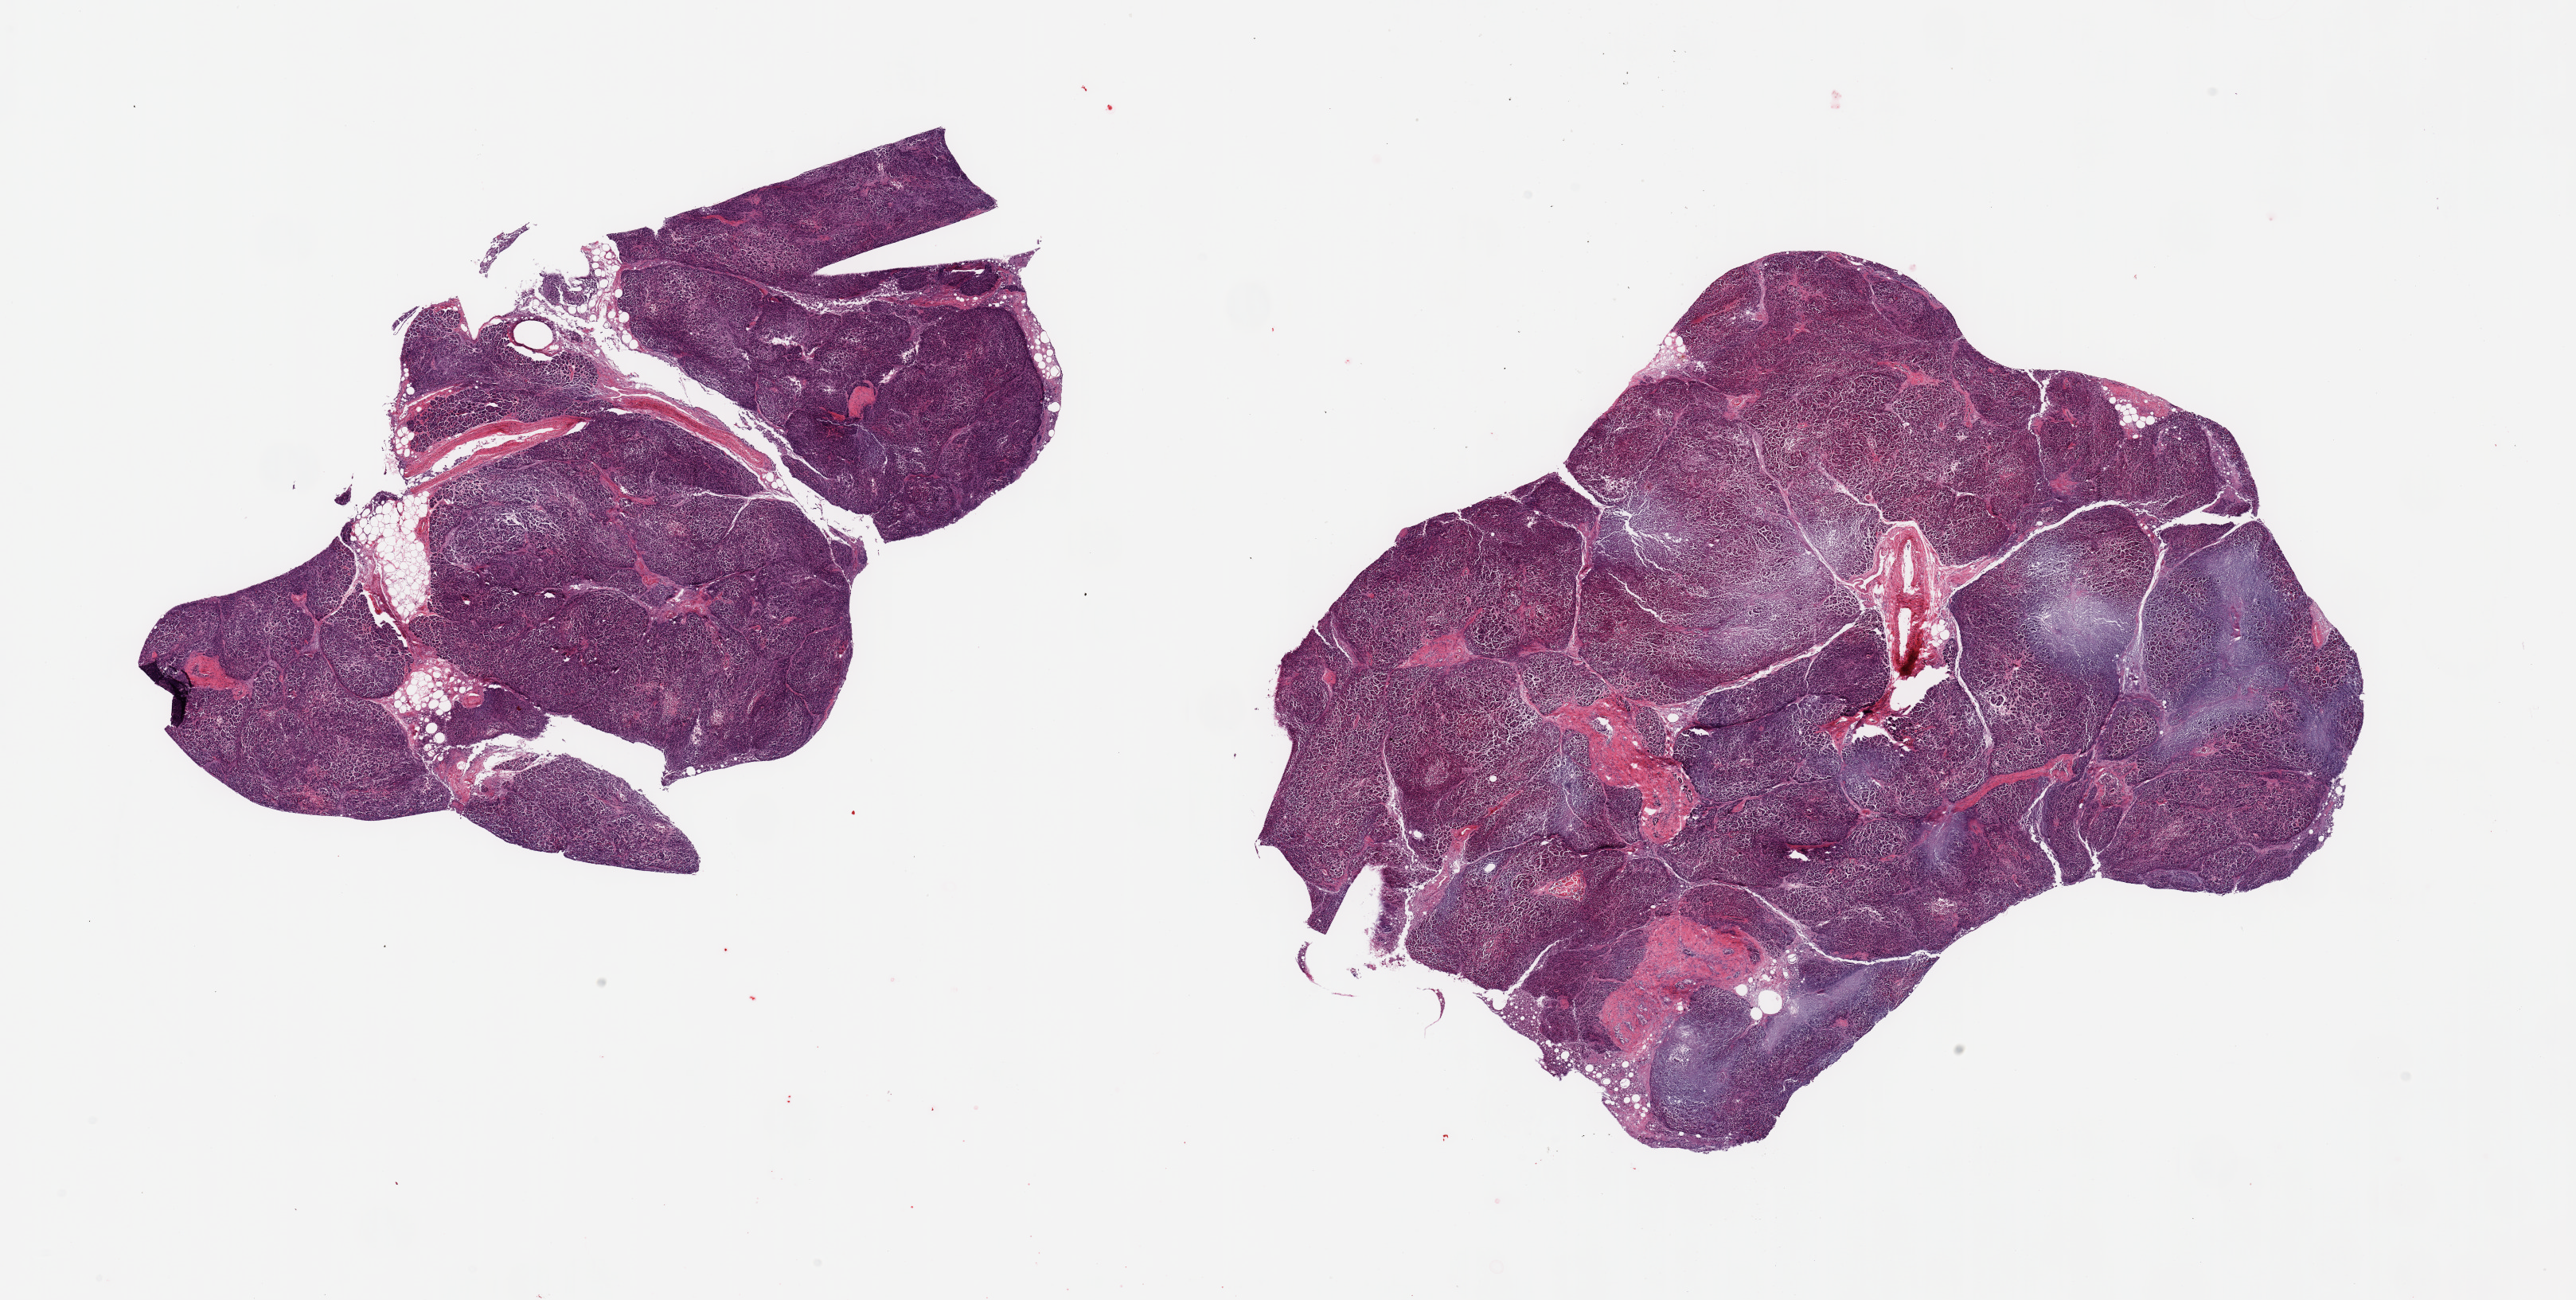
Hematoxylin and eosin (H&E) whole-slide image — shown as a low-resolution overview of the whole scanned area (about 25.6 x 12.9 mm, from a 20x scan), PAXgene-fixed, paraffin-embedded tissue, sampled site (target tissue): pancreas, tissue donor sample. Donor sex: male.
• pathologist's review note for this sample: 2 pieces; severe autolysis, saponification